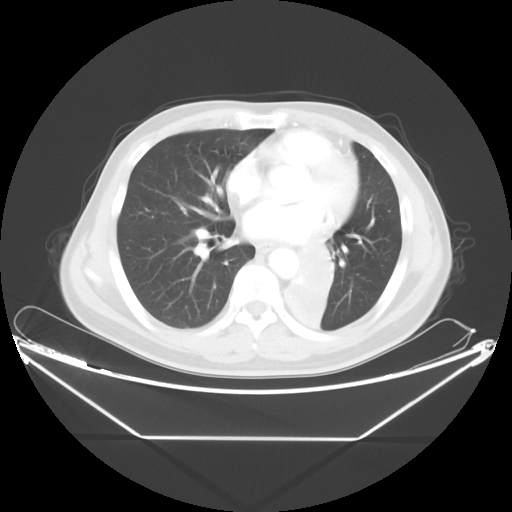
Chest CT, one axial slice. Position 20 of 48 along the scan axis. Reconstruction kernel STANDARD. 120 kVp. Lung window (W 1500 / L -600 HU). 512 × 512 image matrix, field of view 438 × 438 mm. Patient: male, 58 years. From the clinical record (not read from this slice): clinical TNM (as recorded): T3 N3 M0.
Annotated regions visible in this slice (rectangle marked by the reading radiologist):
- lung tumour (recorded histology: squamous cell carcinoma): bounding box [x1, y1, x2, y2] px = [286, 246, 337, 336]